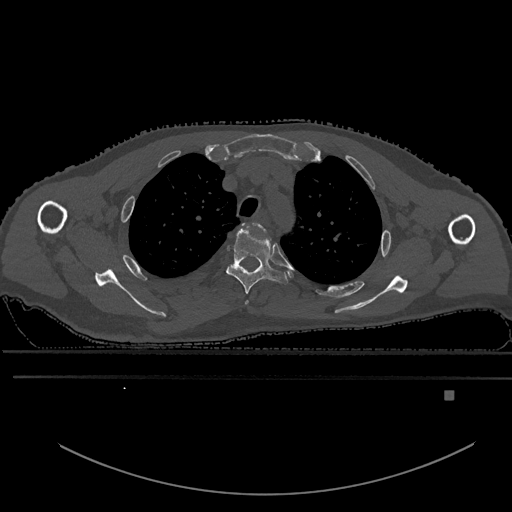
CT including the spine, one axial slice; slice 453 of 969 in the series (ordered by position); bone window (W 1800 / L 400 HU); 0.5 mm slice thickness; 512 × 512 image matrix, field of view 456 × 456 mm. Patient: male, 82 years. Case-level facts recorded for this patient, not image findings: primary cancer: prostate.
Annotated regions visible in this slice (semi-automatically segmented with operator editing):
- T2 vertebra: box from (x=241, y=222) to (x=265, y=304) px
- T3 vertebra: (x=226, y=222)–(x=289, y=294)